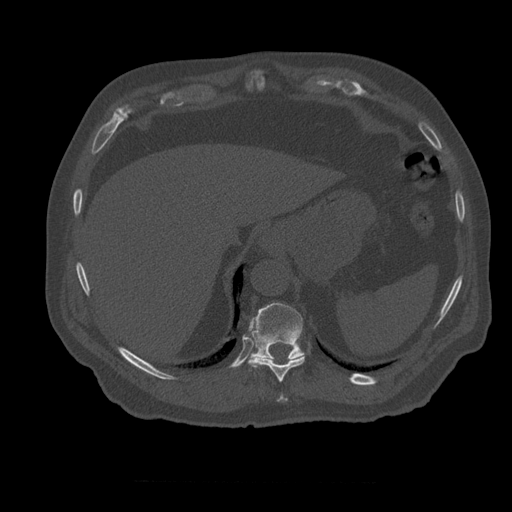
CT including the spine, one axial slice; reconstruction kernel STANDARD; 120 kVp; bone window (W 1800 / L 400 HU); 512 × 512 image matrix, field of view 407 × 407 mm. Patient age 73 years. From the clinical record (not read from this slice): primary cancer: prostate; vertebrae with lytic lesions (as recorded): L2.
Structures marked on this image (semi-automatically segmented with operator editing):
- T10 vertebra: bounding box [x1, y1, x2, y2] px = [249, 344, 305, 382]
- T11 vertebra: [249, 303, 305, 368]
- T9 vertebra: [279, 396, 287, 402]